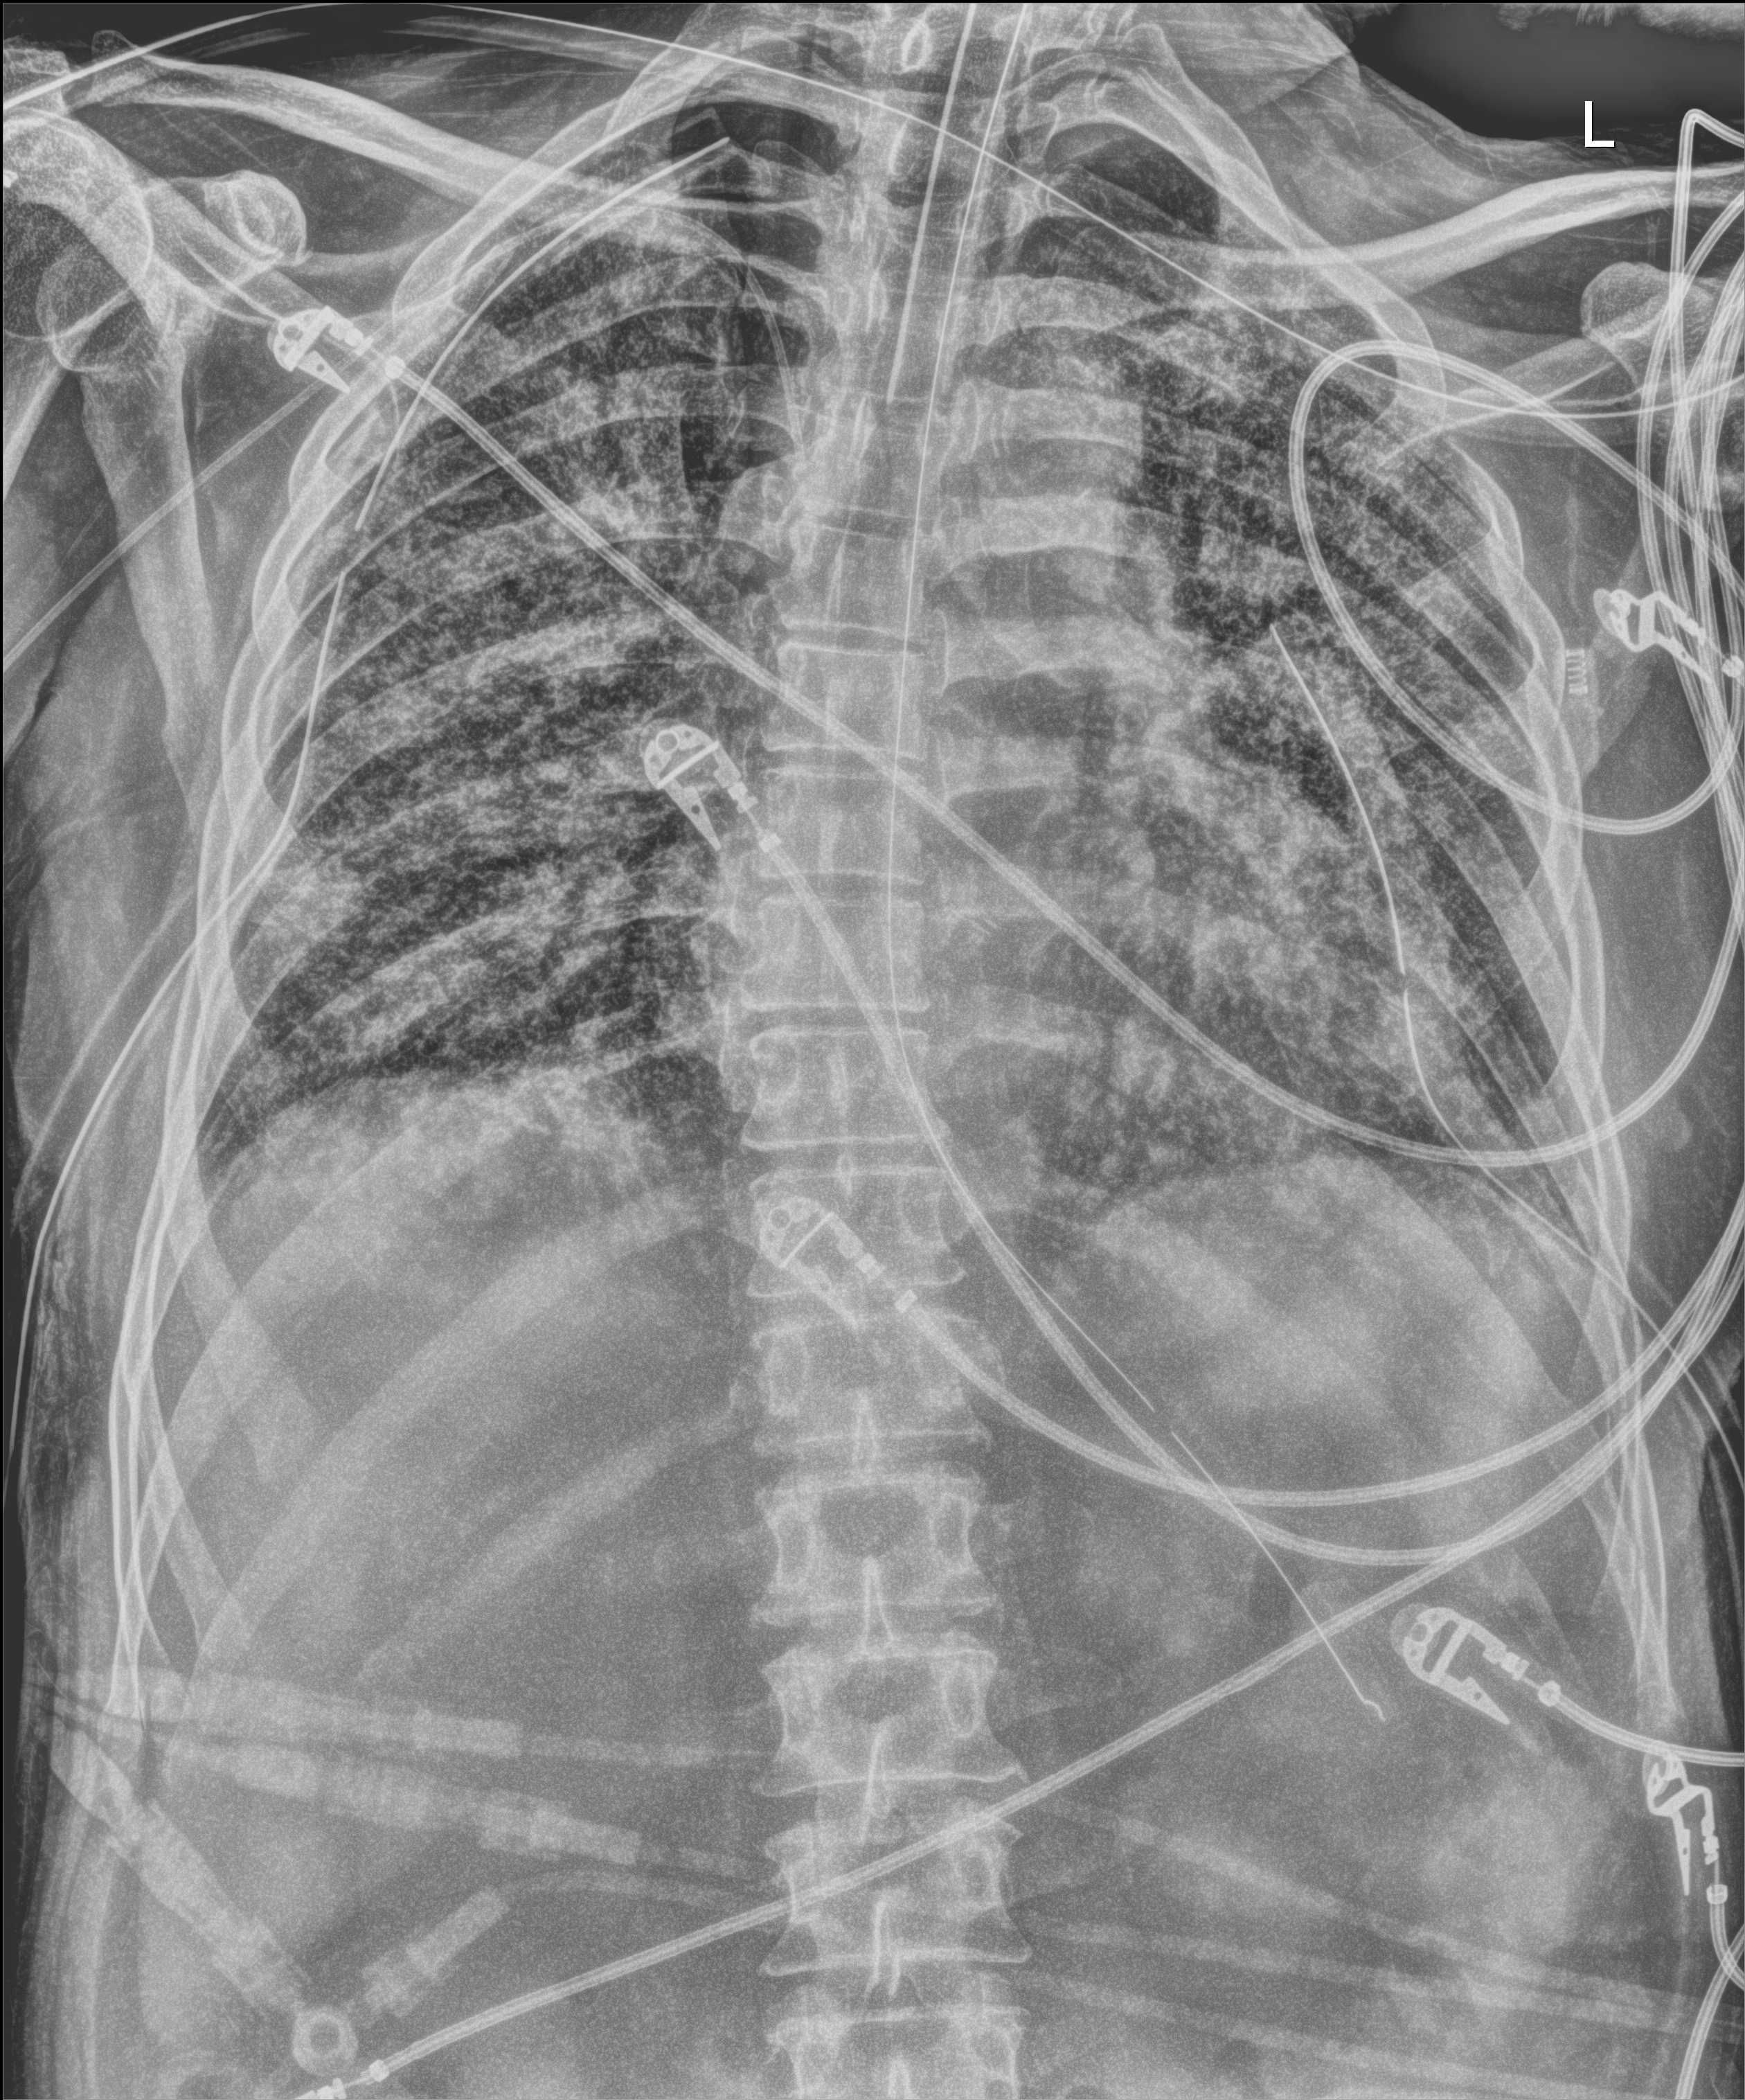
Chest radiograph (digital radiography), anteroposterior (AP) projection. Patient hospitalised with COVID-19; male, aged 60–74 years.
Admission-level facts for this patient (not findings on this image; timing relative to this image not recorded): admitted to intensive care during this hospital stay: yes; other chronic lung disease (admission record): yes.